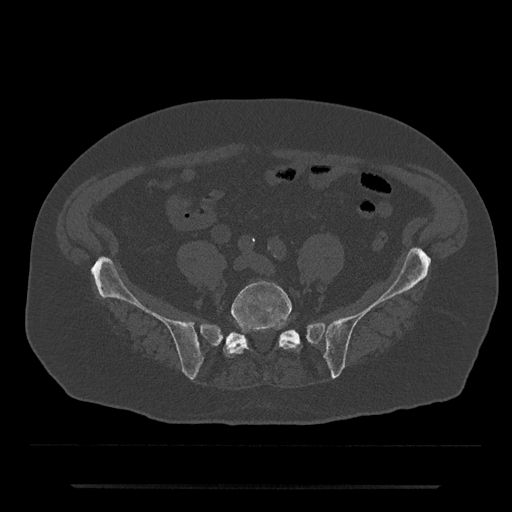
CT including the spine, one axial slice; slice 268 of 797 in the series (ordered by position); reconstruction kernel Br40s/3; 120 kVp; bone window (W 1800 / L 400 HU); 0.5 mm slice thickness; 512 × 512 image matrix, field of view 434 × 434 mm. Patient: male, 80 years. From the clinical record (not read from this slice): primary cancer: prostate; vertebrae with lytic lesions (as recorded): L1, T11.
Structures marked on this image (semi-automatic segmentation, software-assisted and operator-edited):
- L5 vertebra: bounding box (x1, y1, x2, y2) in pixels: (223, 281, 299, 357)